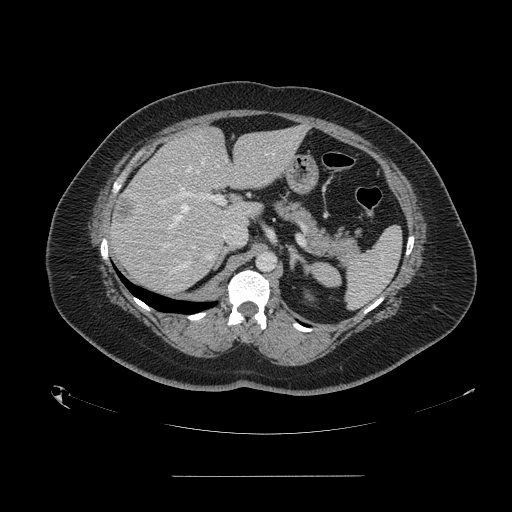
Contrast-enhanced abdominal CT, one axial slice. Slice 96 of 164 in the series (ordered by position). Soft-tissue window (W 400 / L 40 HU). 512 × 512 image matrix, field of view 495 × 495 mm. Female patient, age 52 years. From the clinical record (not read from this slice): diagnosis: colorectal cancer liver metastases, imaged before liver resection; multiple liver metastases: yes; largest metastasis: 3.5 cm; chemotherapy before resection: no.
Outlined on this slice (outlined manually by an expert reader):
- hepatic veins: bounding box (x1, y1, x2, y2) in pixels: (169, 152, 273, 228)
- liver: (111, 127, 305, 293)
- planned liver remnant (the part of the liver to remain after resection): (175, 127, 304, 227)
- portal vein (with intrahepatic branches): (159, 169, 225, 248)
- liver metastasis: (192, 256, 204, 273)
- liver metastasis: (116, 200, 133, 226)